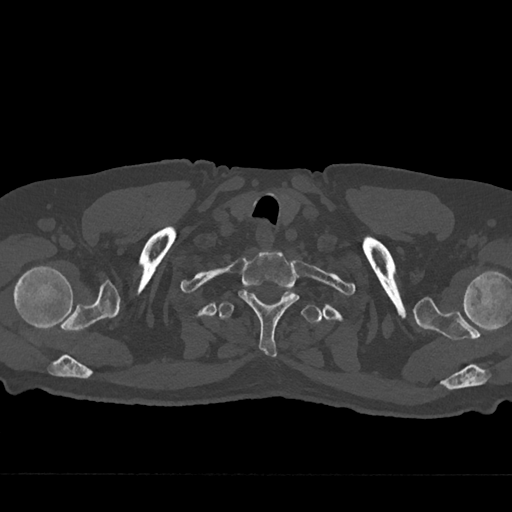
CT including the spine, one axial slice; slice 650 of 797 in the series (ordered by position); reconstruction kernel Br40s/3; 120 kVp; bone window (W 1800 / L 400 HU); 512 × 512 image matrix, field of view 377 × 377 mm. Patient: male, 75 years. From the clinical record (not read from this slice): primary cancer: renal.
Annotated regions visible in this slice (semi-automatically segmented with operator editing):
- T1 vertebra: bounding box <238,250,299,357> (left, top, right, bottom; pixels)
- T2 vertebra: <218,289,322,323>